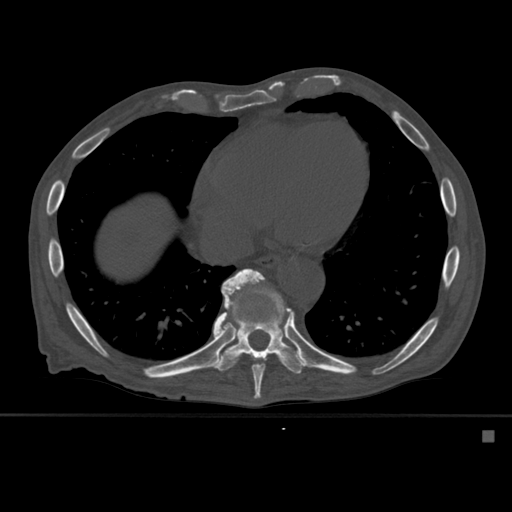
CT including the spine, one axial slice; slice 323 of 527 in the series (ordered by position); bone window (W 1800 / L 400 HU); 1.5 mm slice thickness; 512 × 512 image matrix, field of view 373 × 373 mm. Male patient, age 78 years. From the clinical record (not read from this slice): primary cancer: prostate.
Structures marked on this image (semi-automatic segmentation, software-assisted and operator-edited):
- T10 vertebra: box from (x=213, y=278) to (x=306, y=374) px
- T9 vertebra: (x=221, y=268)–(x=295, y=399)